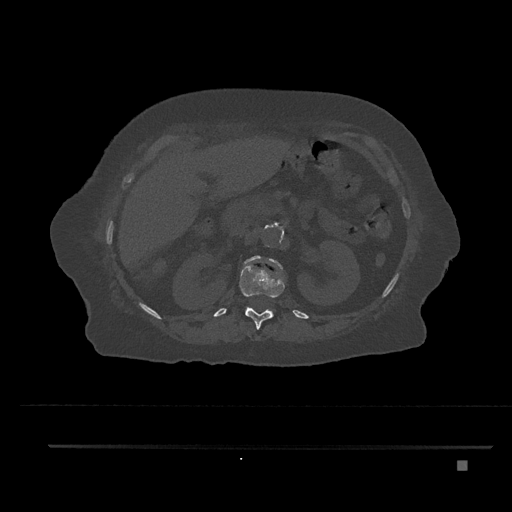
CT including the spine, one axial slice; slice 252 of 797 in the series (ordered by position); reconstruction kernel Br40s/3; 120 kVp; bone window (W 1800 / L 400 HU); 0.5 mm slice thickness; 512 × 512 image matrix, field of view 437 × 437 mm. Female patient, age 76 years. From the clinical record (not read from this slice): primary cancer: lung.
Outlined on this slice (semi-automatic segmentation, software-assisted and operator-edited):
- L1 vertebra: bounding box <242,255,284,308> (left, top, right, bottom; pixels)
- T12 vertebra: <240,264,285,330>